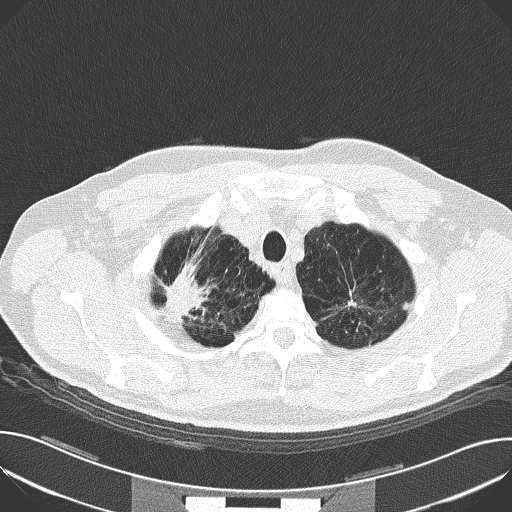
Chest CT (low-dose screening protocol), one axial image; baseline screening round; lung window (W 1500 / L -600 HU); 2 mm slice thickness; lung (sharp) reconstruction kernel (B50f); 120 kVp; 512 × 512 image matrix, field of view 380 × 380 mm. Male participant, aged 59 years at enrolment. Current smoker at enrolment.
Expert-annotated lung lesion, box from (x=155, y=260) to (x=222, y=331) px. The screening reader recorded 4 non-calcified nodules or masses ≥4 mm on this exam; which of them this box marks is not recorded. Participant outcome: lung cancer diagnosed 44 days after this screen — squamous cell carcinoma, NOS, right upper lobe, moderately differentiated (G2), stage IA (AJCC 6th edition), 30 mm at pathology.